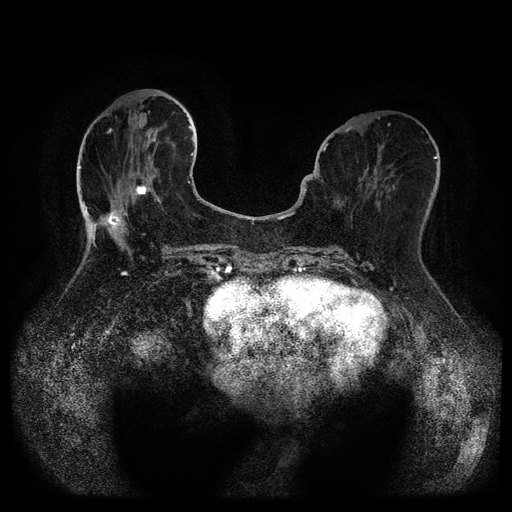
Breast MRI (dynamic contrast-enhanced, multi-phase), one axial slice. Slice 39 of 116 in the series (ordered by position). Dynamic contrast-enhanced series, time point 2 of 5 at this slice position (early post-contrast). 1.5 T. TE 2.6 ms, TR 5.3 ms. 2 mm slice thickness. 512 × 512 image matrix. Female patient, age 75 years.
Outlined on this slice (semi-automatic segmentation, software-assisted and operator-edited):
- breast lesion (labelled benign in the annotation): bounding box (x1, y1, x2, y2) in pixels: (132, 182, 152, 200)
- breast lesion (labelled benign in the annotation): (105, 212, 122, 230)